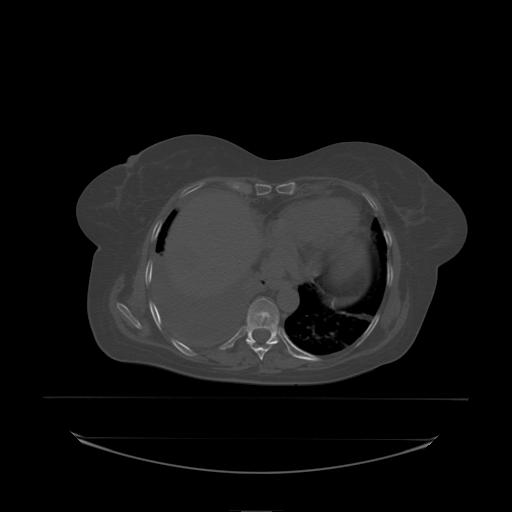
CT including the spine, one axial slice; slice 128 of 242 in the series (ordered by position); bone window (W 1800 / L 400 HU); 2.5 mm slice thickness; 512 × 512 image matrix, field of view 500 × 500 mm. Female patient, age 53 years. Case-level facts recorded for this patient, not image findings: primary cancer: lung.
Annotated regions visible in this slice (semi-automatically segmented with operator editing):
- T9 vertebra: bounding box [x1, y1, x2, y2] px = [246, 298, 279, 338]